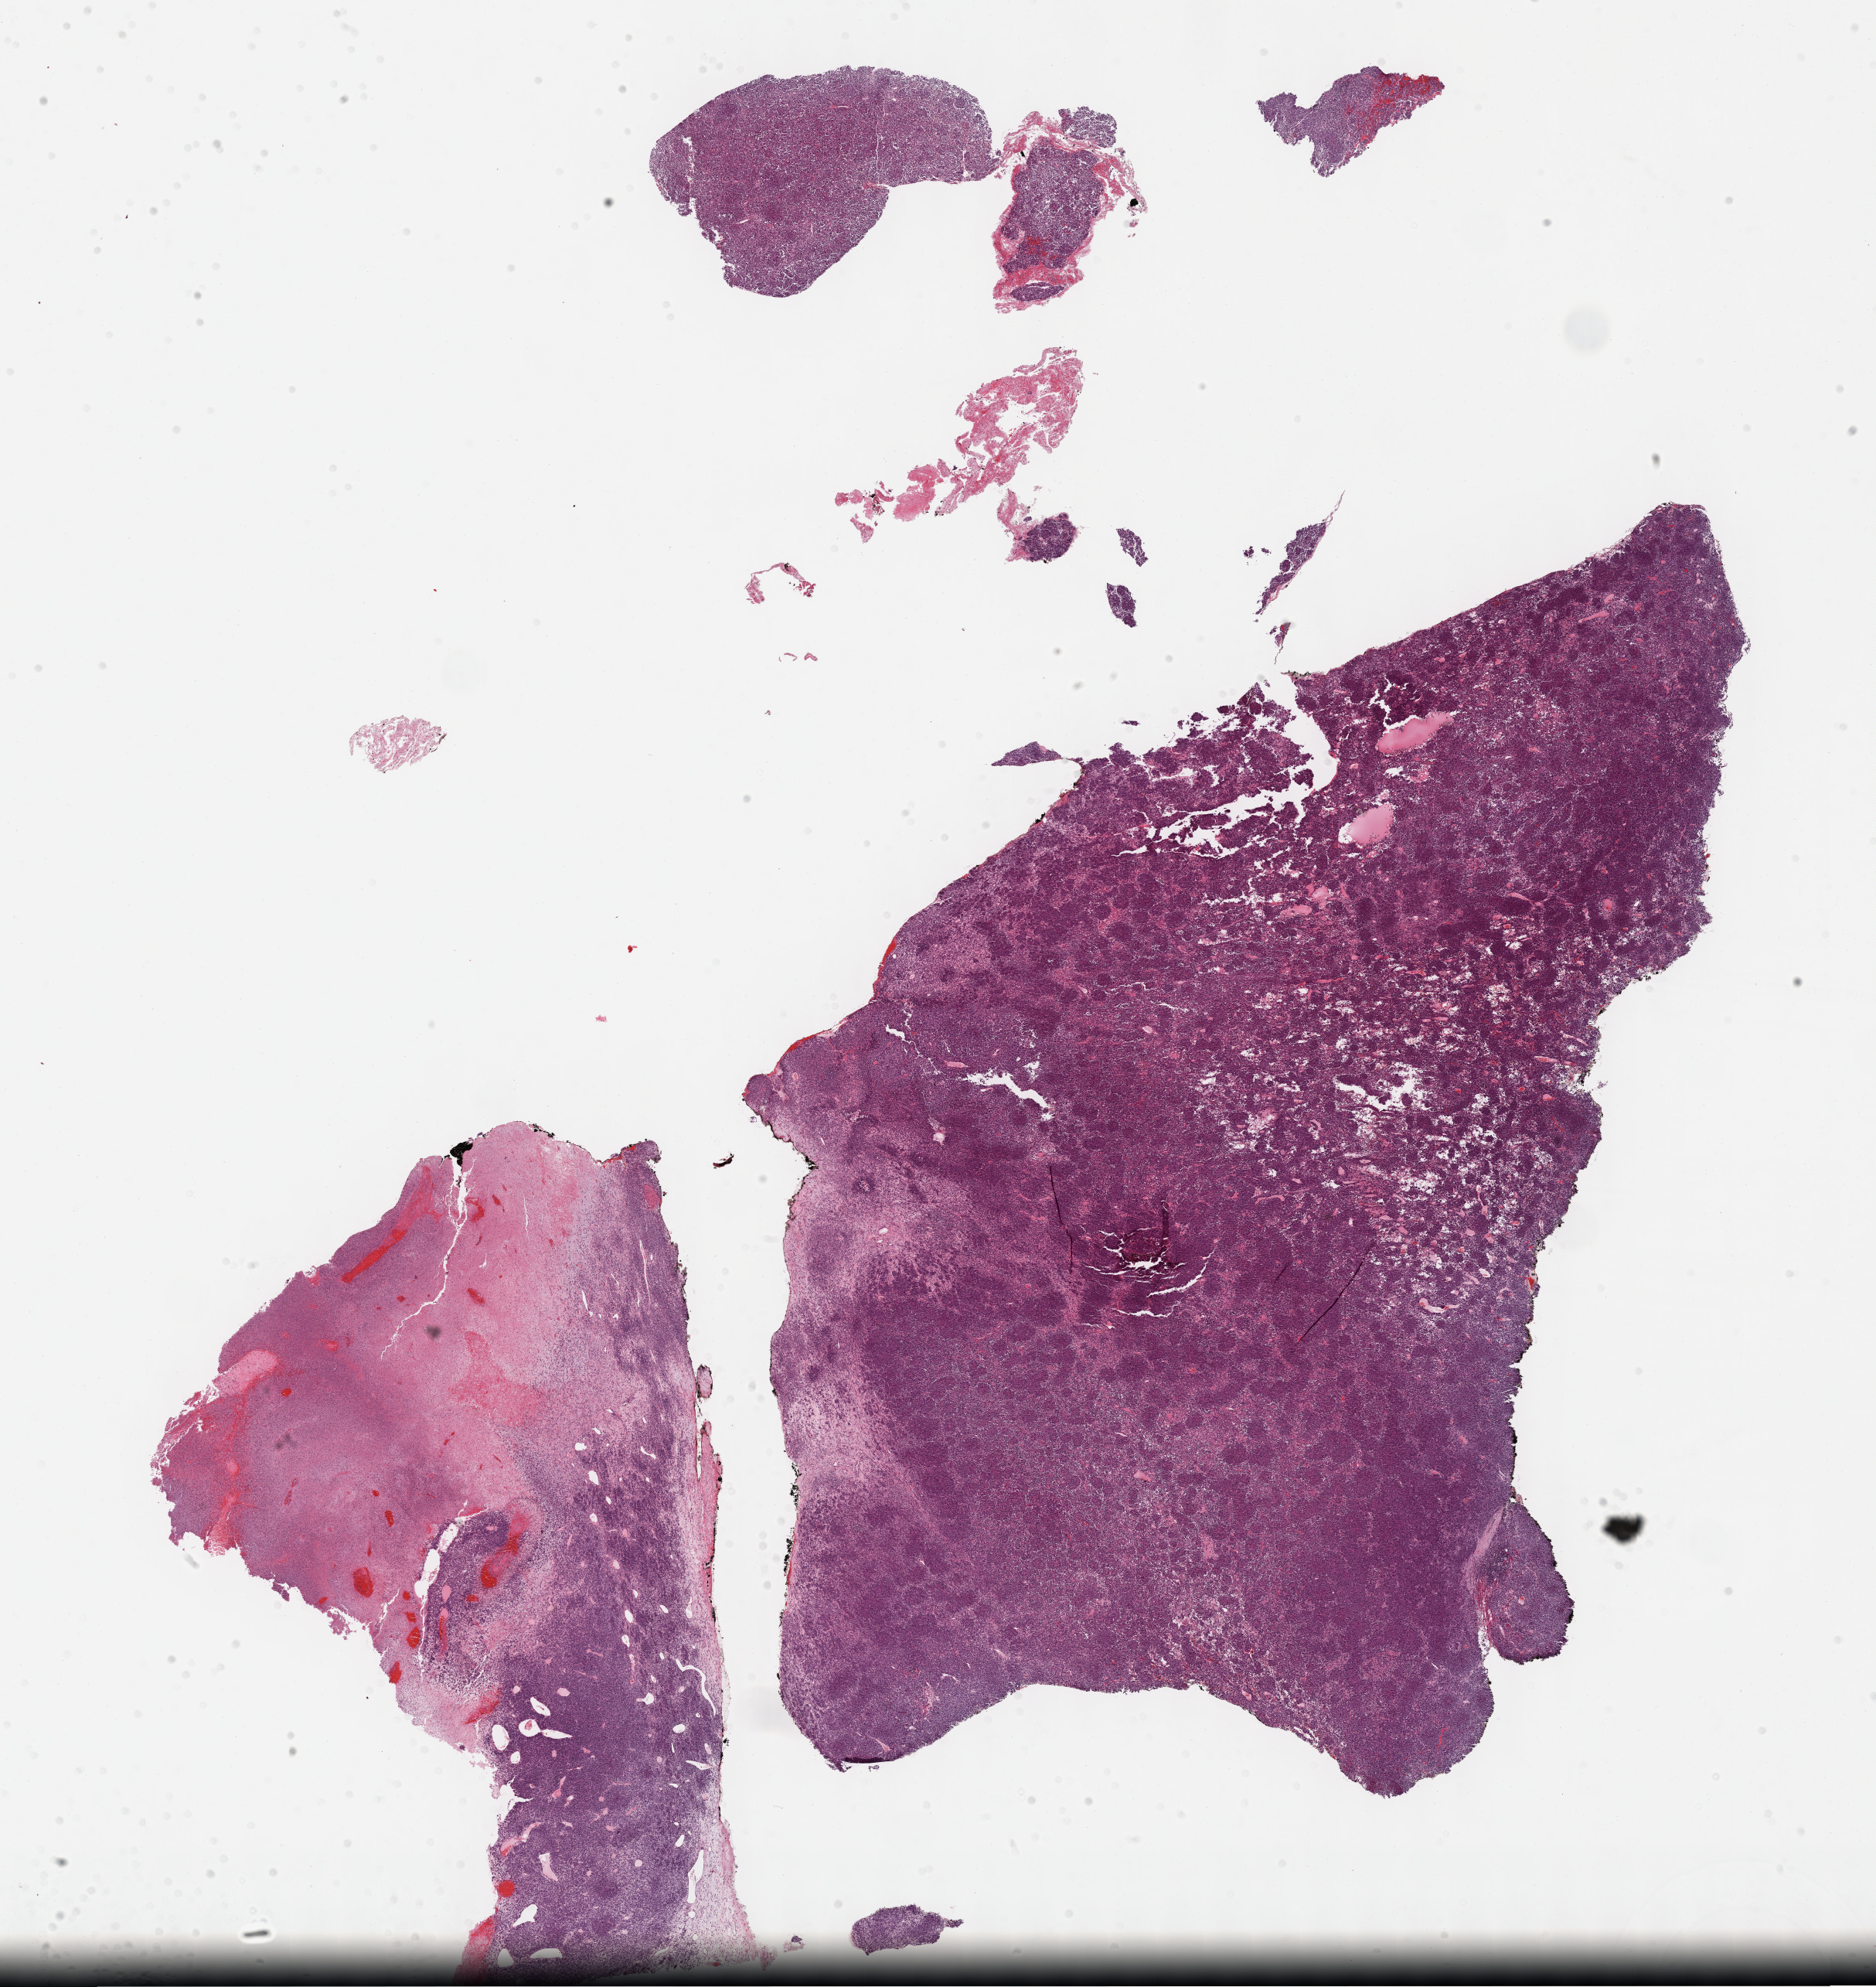
Whole-slide histology image, H&E-stained, a low-resolution overview of the entire scanned area, about 19.6 x 20.8 mm (from a 40x scan), formalin-fixed paraffin-embedded (FFPE) diagnostic section, metastatic tumour sample, sampled site: liver. Patient: female, age at initial diagnosis 43 years.
- this section: metastatic tumour tissue
- patient diagnosis: Malignant melanoma, NOS